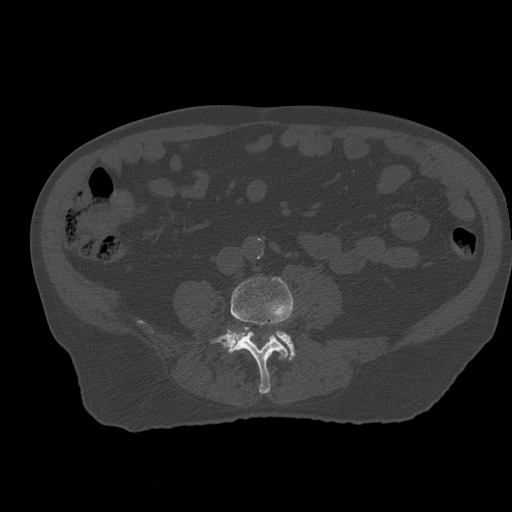
CT including the spine, one axial slice; position 160 of 399 along the scan axis; reconstruction kernel STANDARD; bone window (W 1800 / L 400 HU); 1.25 mm slice thickness; 512 × 512 image matrix. Patient age 73 years. From the clinical record (not read from this slice): primary cancer: prostate.
Outlined on this slice (semi-automatically segmented with operator editing):
- L4 vertebra: bounding box [x1, y1, x2, y2] px = [210, 278, 294, 394]
- L5 vertebra: [230, 327, 296, 360]